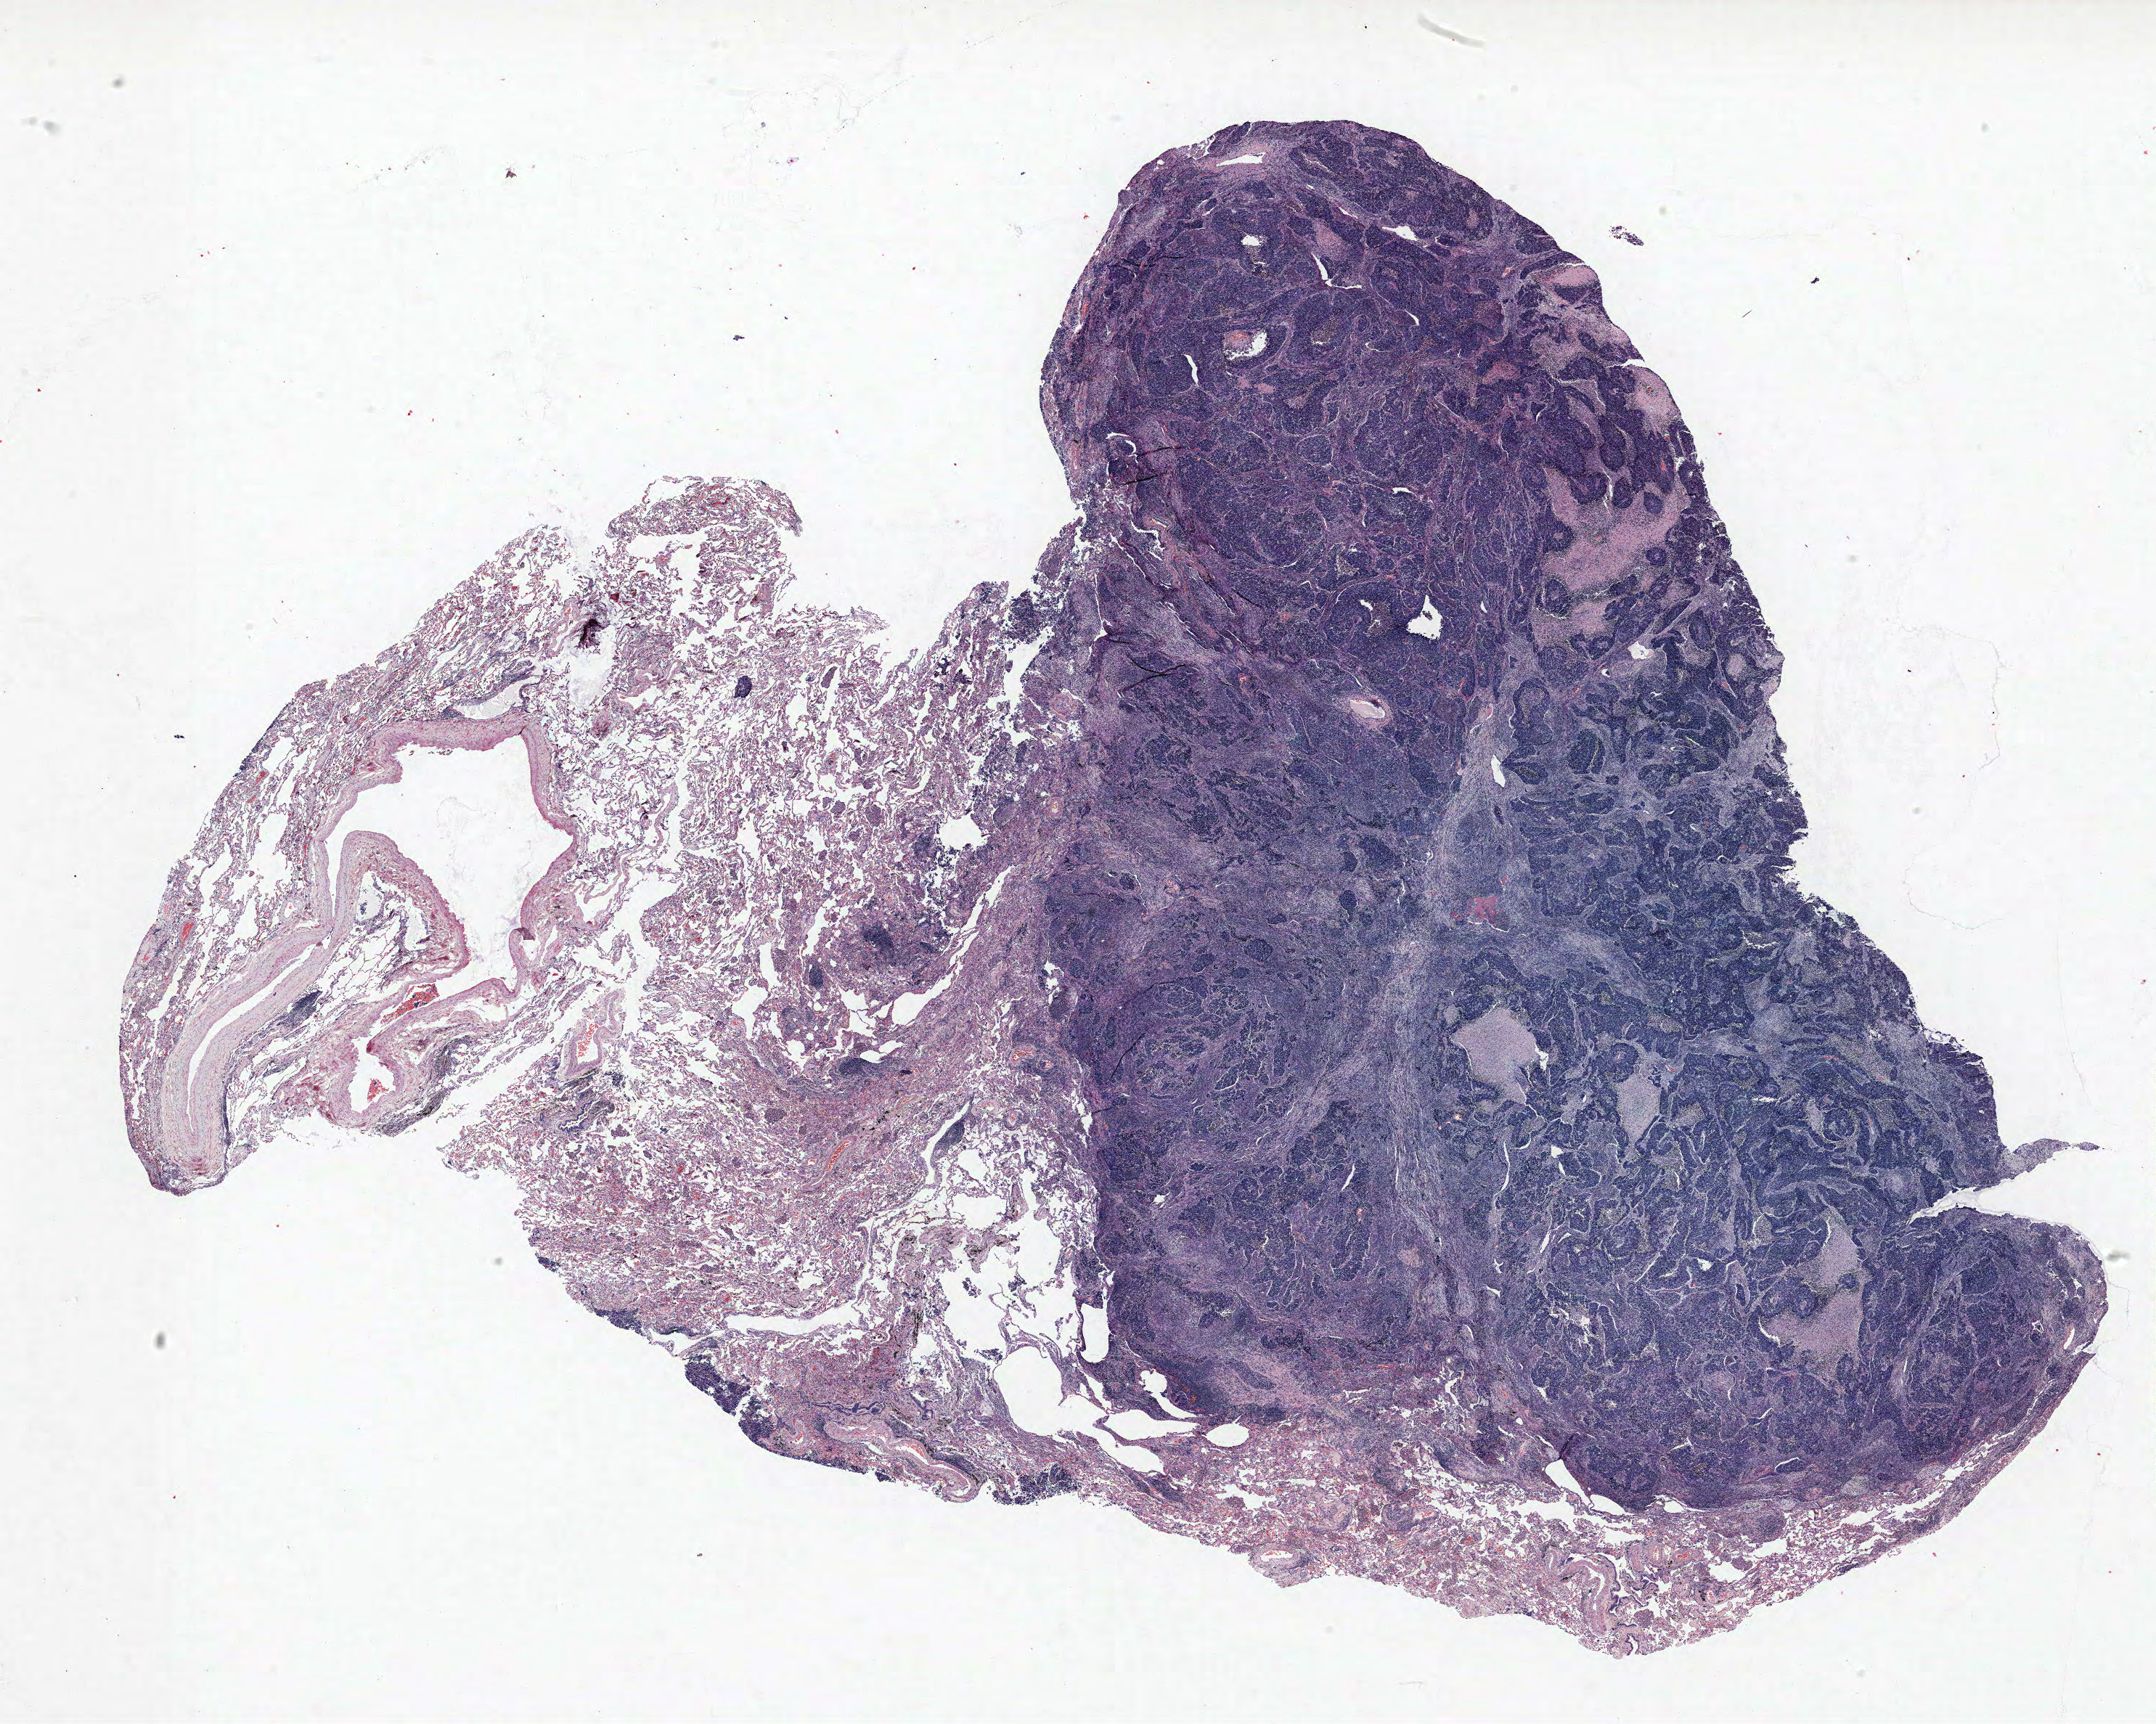
Whole-slide histology image, Hematoxylin and eosin (H&E) stained — low-resolution overview of the scanned area, about 23.8 x 19.0 mm. Formalin-fixed paraffin-embedded (FFPE) section. Lung tissue. Male, age 73 at enrolment. Current smoker at enrolment. Grade: poorly differentiated (G3).
* primary tumour location (clinical record): left upper lobe
* tumour size (pathology): 26 mm
* participant's lung-cancer diagnosis: Neuroendocrine carcinoma, NOS
* stage (AJCC 6th edition): IA